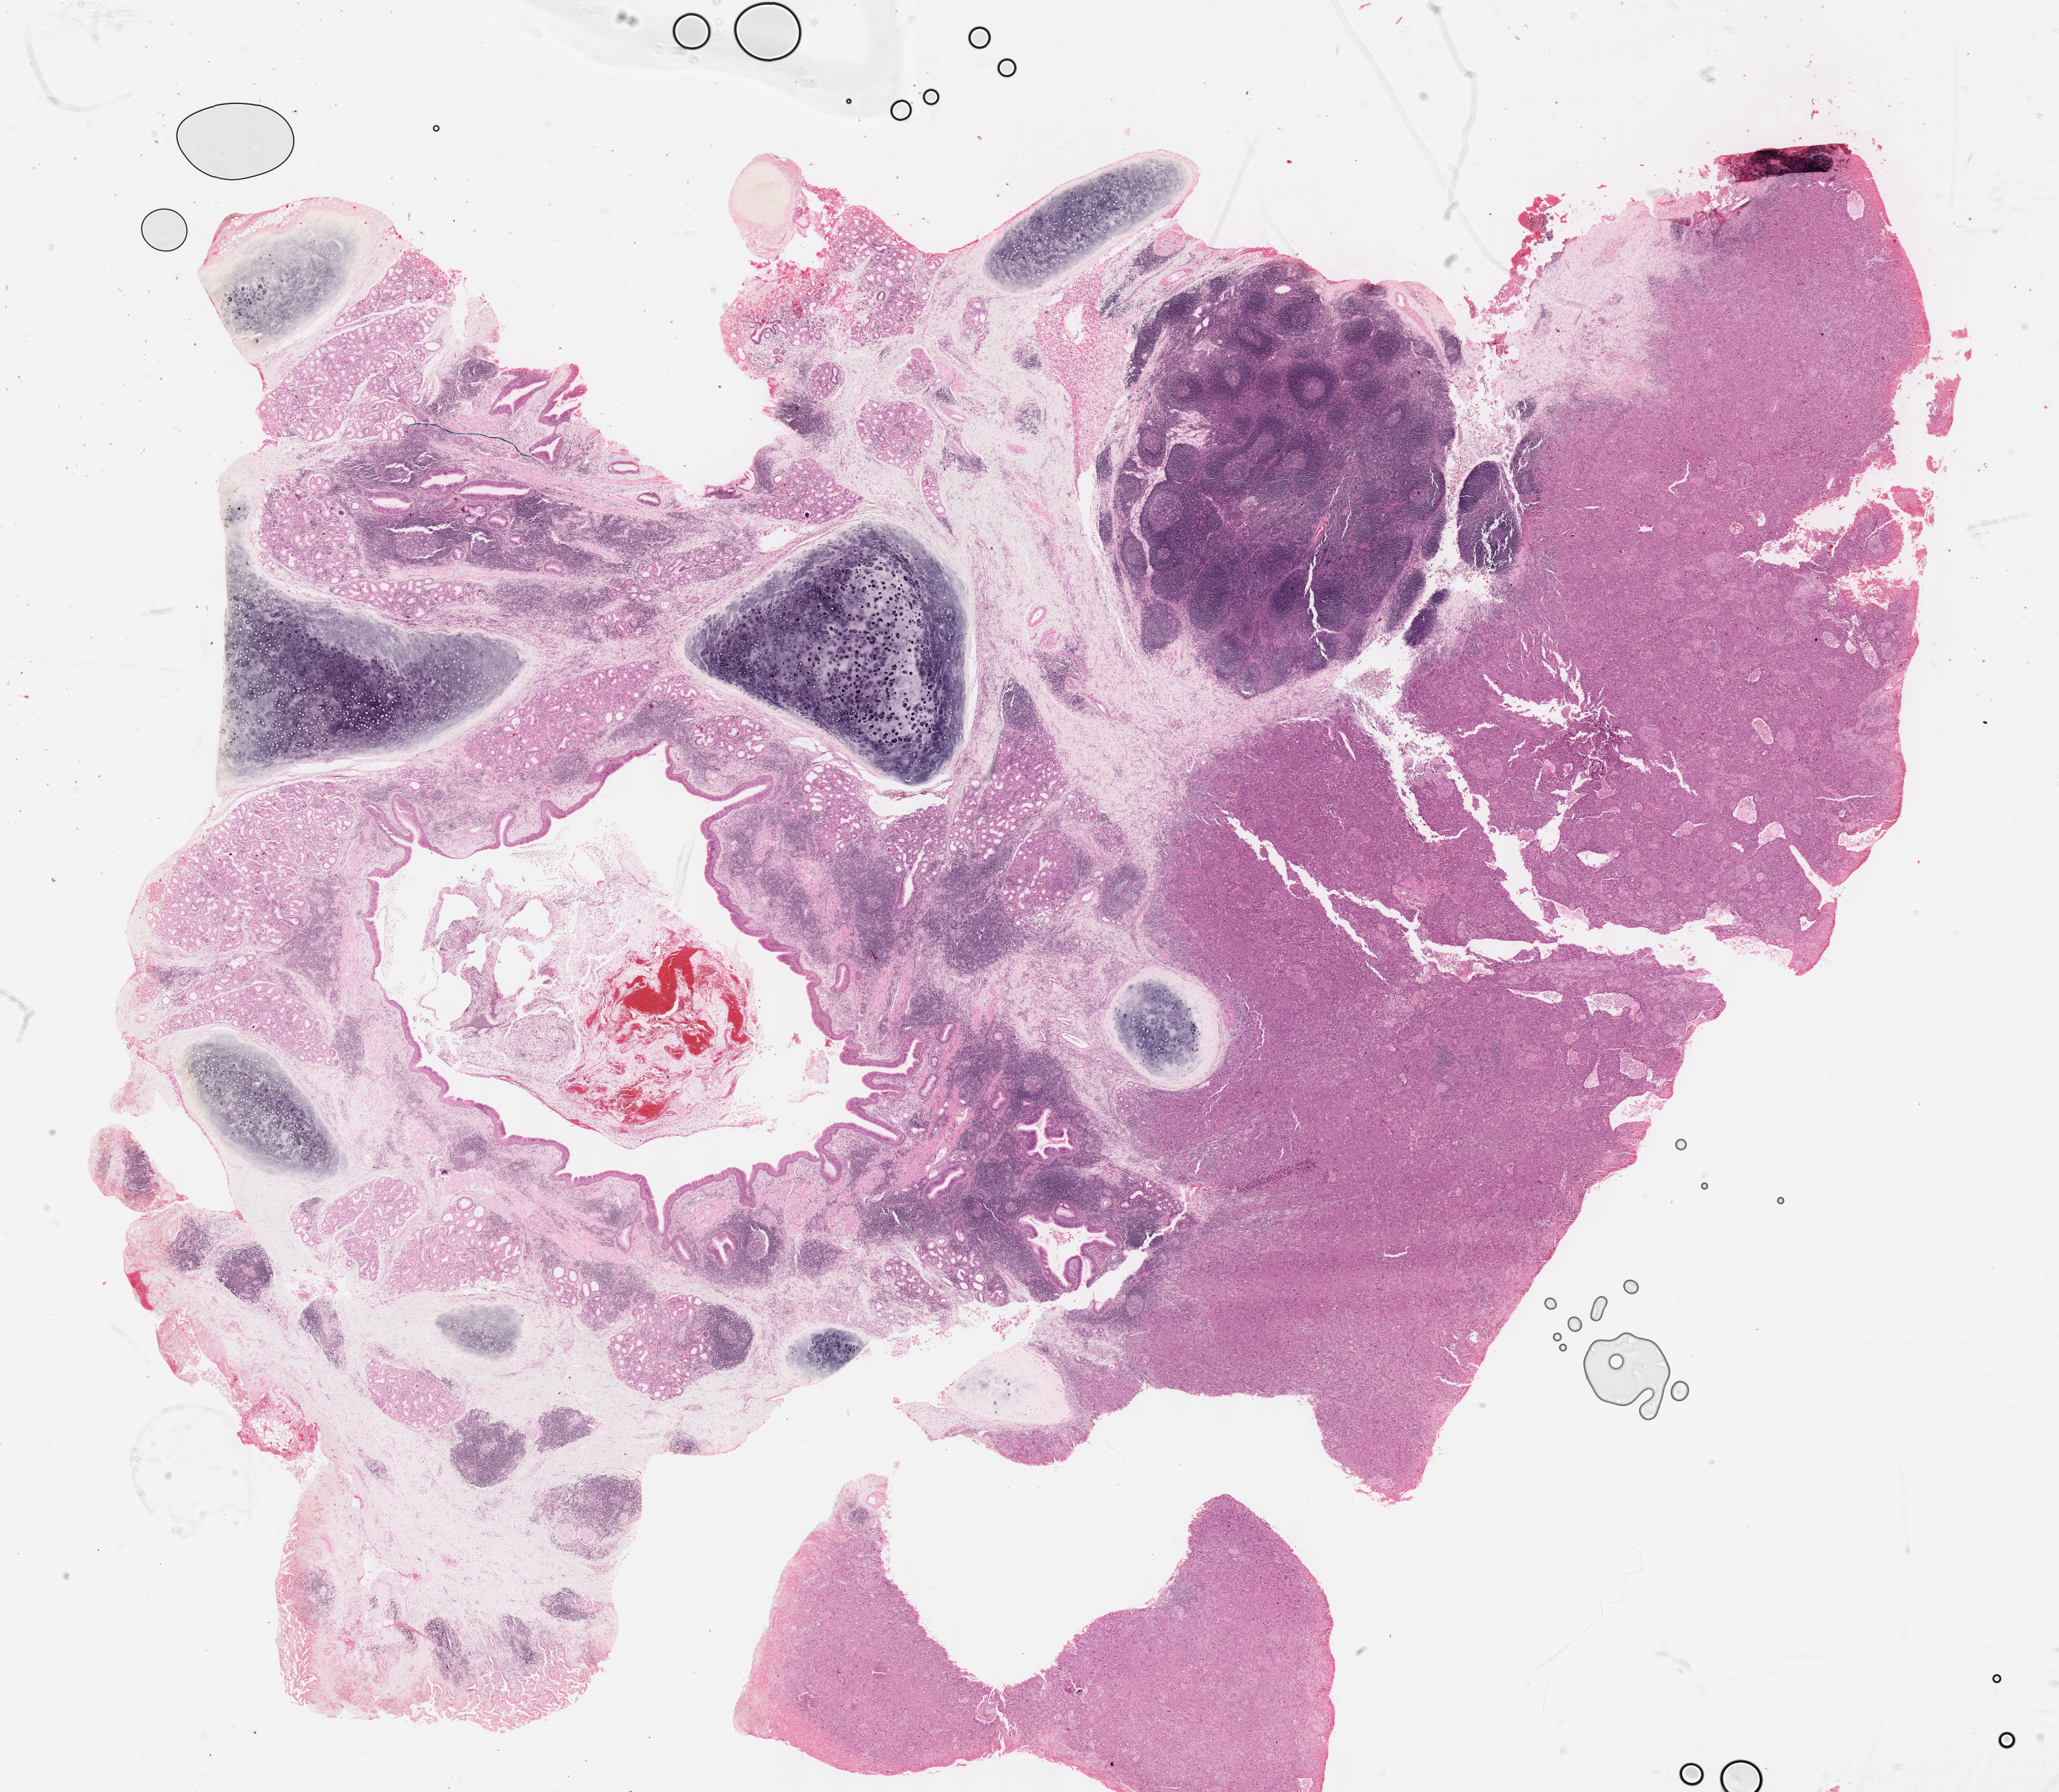
Hematoxylin and eosin (H&E) stained whole-slide image — shown as a low-resolution overview of the whole scanned area (about 24.1 x 21.0 mm, acquisition: 40x scan). Formalin-fixed paraffin-embedded (FFPE) diagnostic section. Primary tumour sample from the lung. Male, age 40 years at initial diagnosis.
* TNM: T2 N0 M0
* diagnosis: Squamous cell carcinoma, NOS
* AJCC pathologic stage: IB (4th edition)